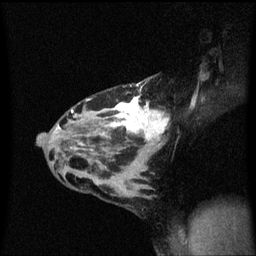
Breast MRI (dynamic contrast-enhanced), one sagittal slice. Slice 36 of 60 in the series (ordered by position). Dynamic contrast-enhanced series, image 2 of 3 at this slice position (ordered by acquisition). 1.5 T. TE 4.2 ms, TR 8.4 ms. 256 × 256 image matrix, field of view 200 × 200 mm. Patient: female, 32 years.
Annotated regions visible in this slice (semi-automatically segmented with operator editing):
- analysis volume of interest (the breast-tissue region the enhancement analysis was run in; not a lesion): bounding box [x1, y1, x2, y2] px = [55, 78, 172, 167]
- tumour enhancement mask (voxels above the 70 % enhancement threshold inside the analysis volume of interest): [59, 84, 169, 151]